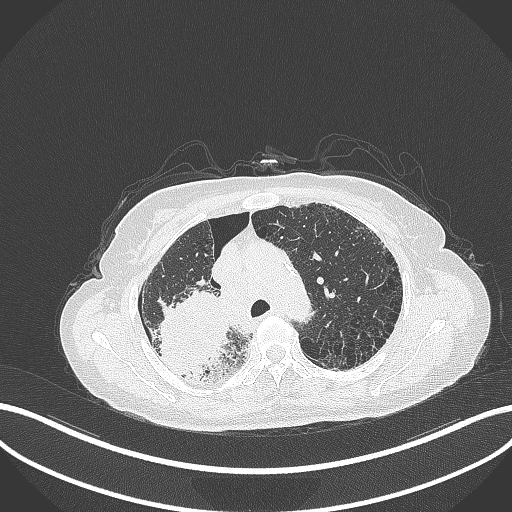
Chest CT, one axial slice; slice 253 of 408 in the series (ordered by position); 120 kVp; lung window (W 1500 / L -600 HU); 1 mm slice thickness; 512 × 512 image matrix. Patient: female, 64 years. Case-level facts recorded for this patient, not image findings: clinical TNM (as recorded): T3 N3 M0.
Annotated regions visible in this slice (bounding box drawn by a radiologist):
- lung tumour (recorded histology: squamous cell carcinoma): bounding box (x1, y1, x2, y2) in pixels: (154, 292, 233, 385)